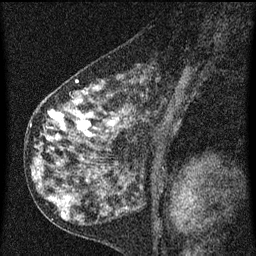
Breast MRI (dynamic contrast-enhanced), one sagittal slice. Slice 34 of 60 in the series (ordered by position). Dynamic contrast-enhanced series, image 2 of 3 at this slice position (ordered by acquisition). 1.5 T. TE 4.2 ms, TR 8 ms. 2 mm slice thickness. 256 × 256 image matrix. Female patient, age 55 years.
Structures marked on this image (semi-automatically segmented with operator editing):
- analysis volume of interest (the breast-tissue region the enhancement analysis was run in; not a lesion): box from (x=42, y=72) to (x=185, y=155) px
- tumour enhancement mask (voxels above the 70 % enhancement threshold inside the analysis volume of interest): (x=49, y=80)–(x=124, y=137)